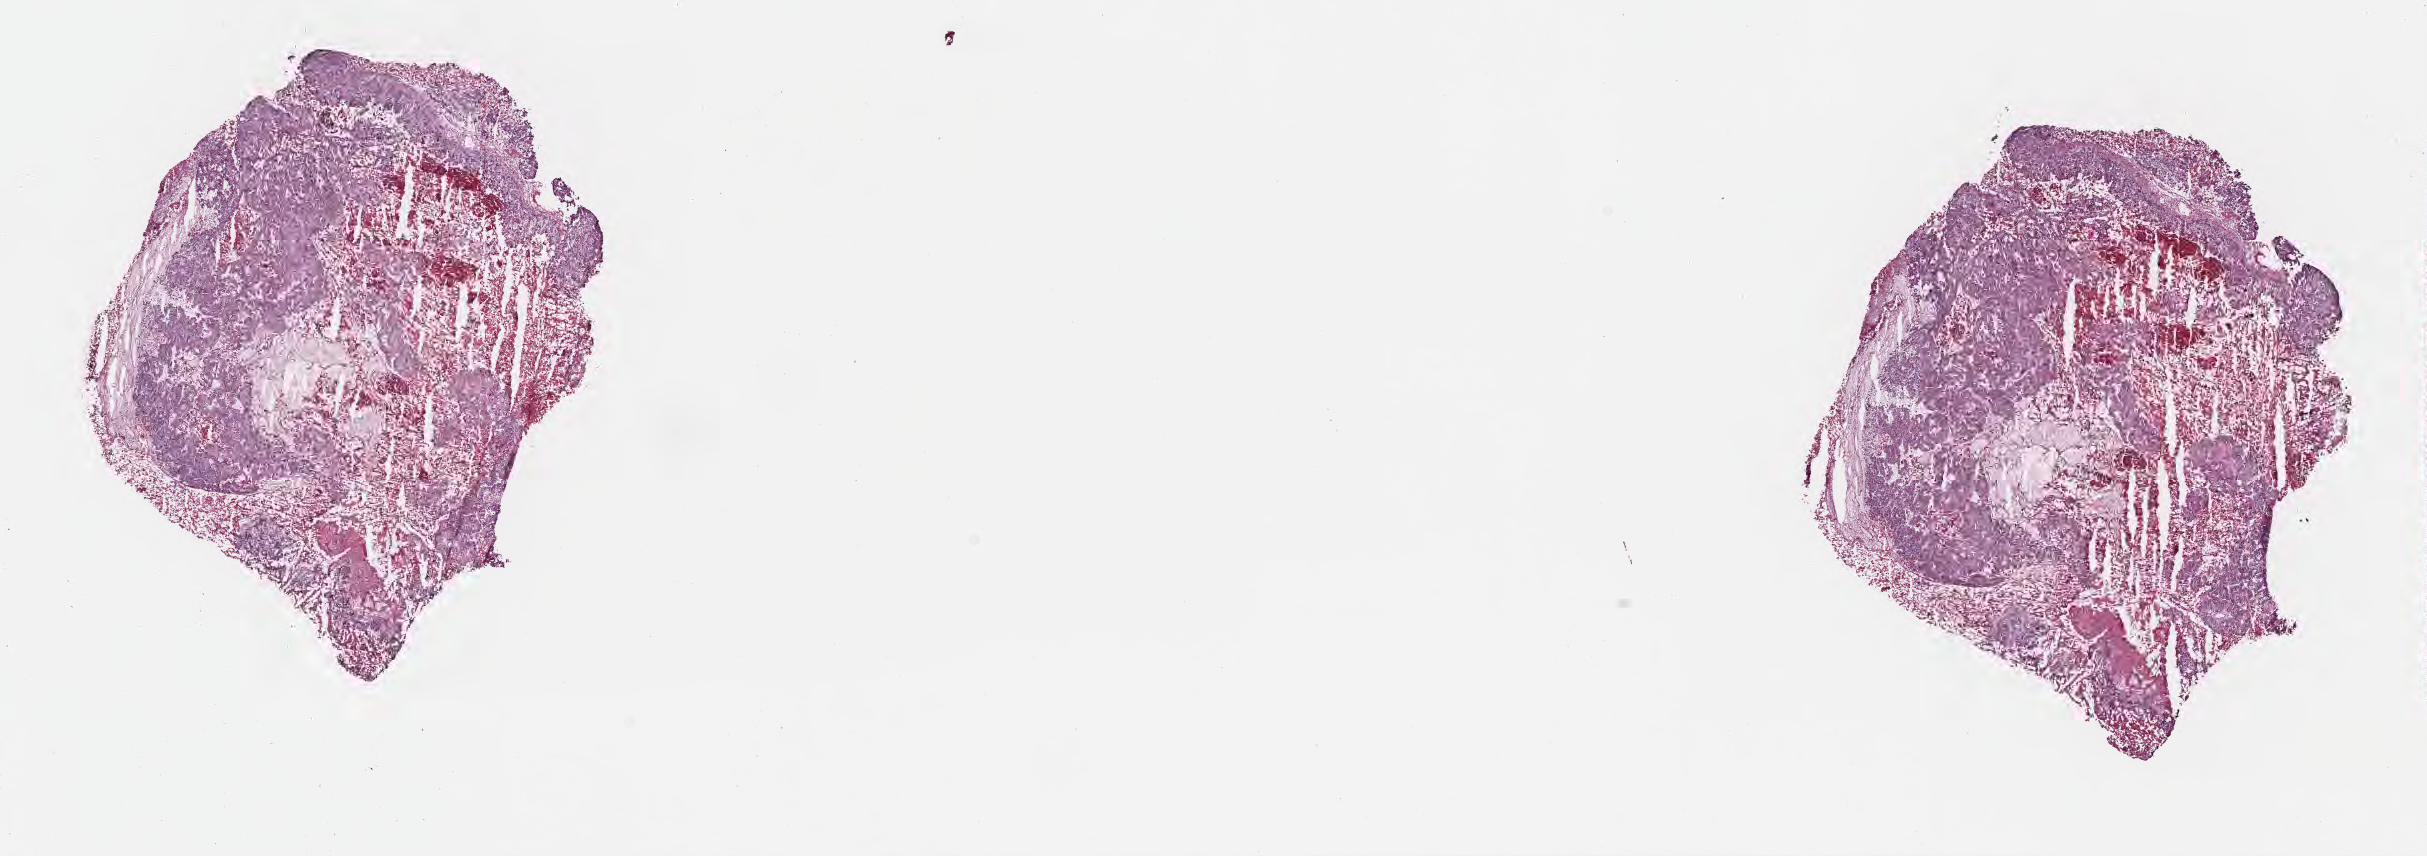
Whole-slide image, H&E stain, low-resolution overview of the scanned area, about 19.6 x 6.9 mm, frozen section, specimen: metastatic tumor tissue, resected from brain. Male patient; age at initial diagnosis 60 years. Slide review estimates, as recorded: tumor cells 52%, tumor nuclei 87%, stromal cells 5%, necrosis 35%, normal cells 8%. Inflammatory infiltration, as recorded: lymphocyte infiltration 3%, monocyte infiltration 0%, neutrophil infiltration 0%.
Patient diagnosis (primary): Adenocarcinoma, NOS.